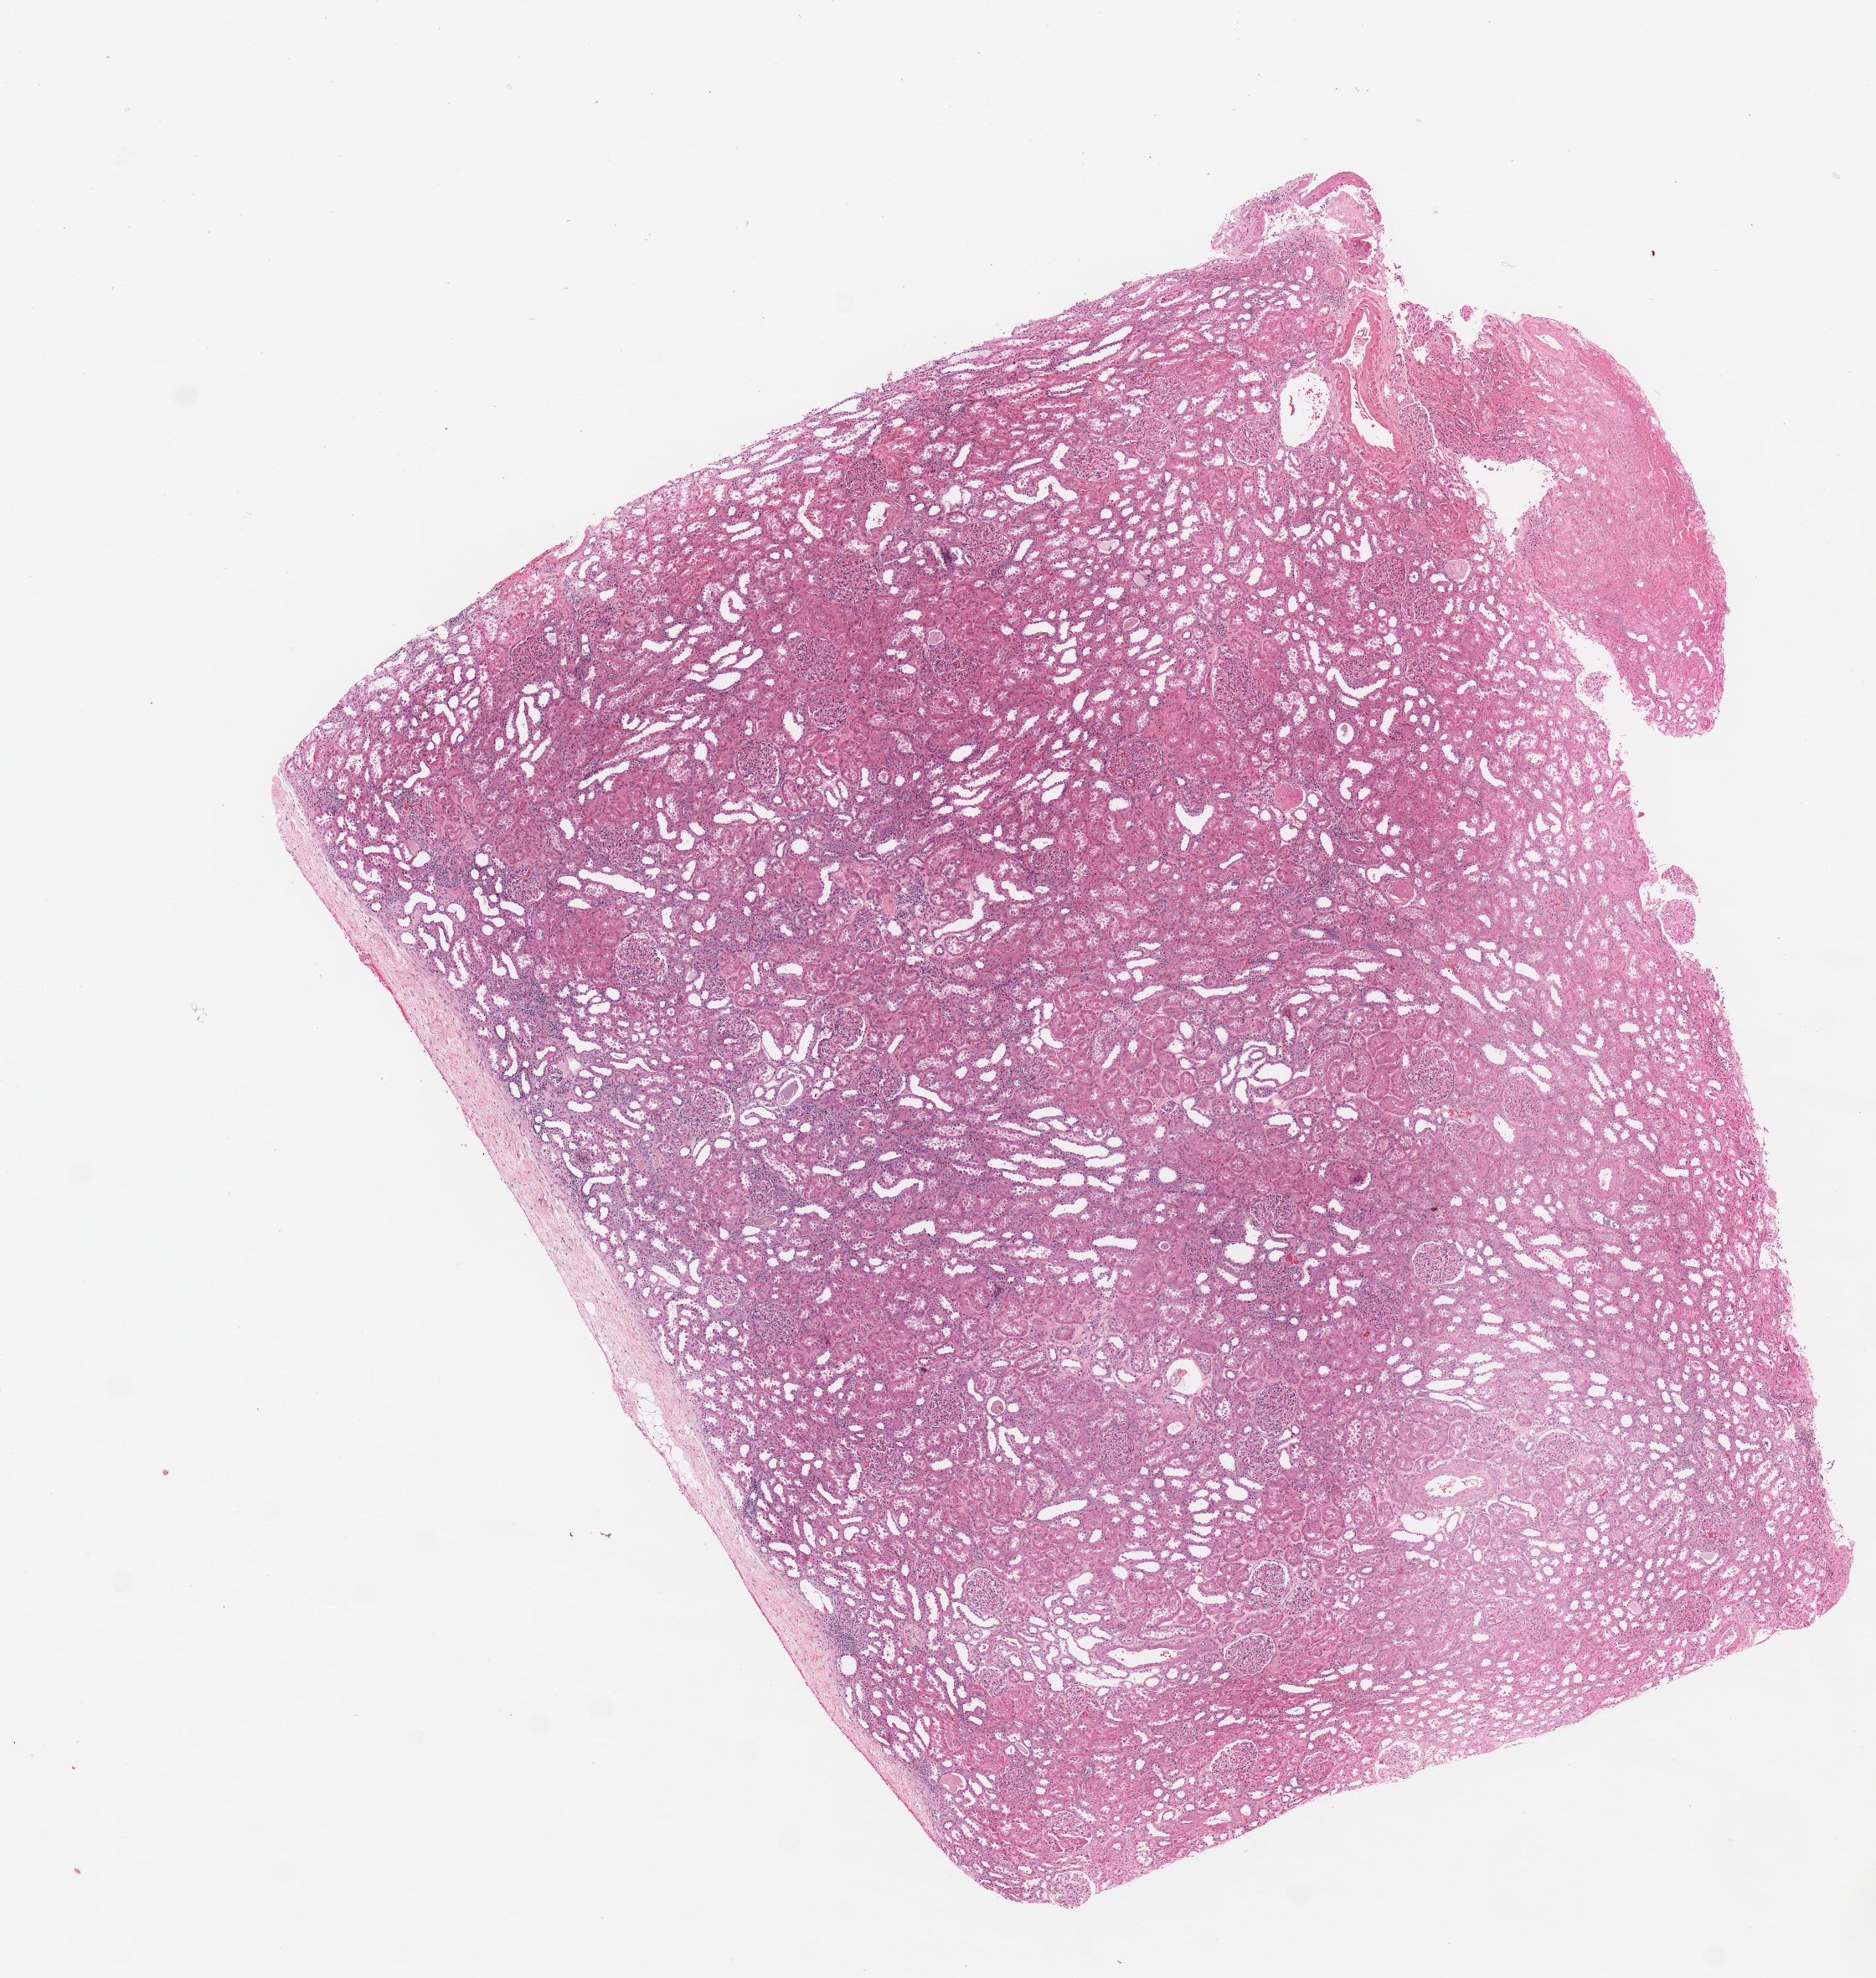
H&E-stained whole-slide image — shown as a low-resolution overview of the whole scanned area (about 8.9 x 9.3 mm). Normal (non-tumour) tissue sample, sampled site: kidney. Patient: male, age 68 years.
This section: normal (non-tumour) tissue from the same patient. Patient diagnosis: Renal cell carcinoma, NOS.